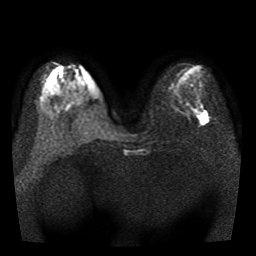
Breast MRI, one axial slice; position 14 of 41 along the scan axis; diffusion-weighted series; image 2 of 3 stored at this slice position (different b-values; order by instance number); 1.5 T; 256 × 256 image matrix, field of view 330 × 330 mm. Female patient.
Outlined on this slice (expert manual segmentation):
- tumour on diffusion-weighted imaging: bounding box <200,112,208,124> (left, top, right, bottom; pixels)